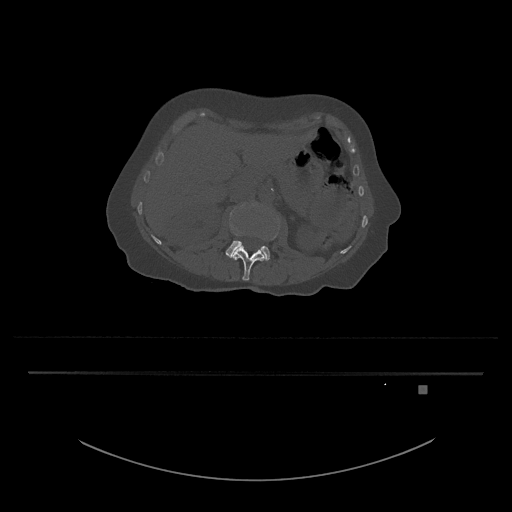
CT including the spine, one axial slice; slice 466 of 797 in the series (ordered by position); 120 kVp; bone window (W 1800 / L 400 HU); 0.5 mm slice thickness; 512 × 512 image matrix, field of view 500 × 500 mm. Female patient, age 57 years. From the clinical record (not read from this slice): primary cancer: cervical.
Structures marked on this image (semi-automatic segmentation, software-assisted and operator-edited):
- L3 vertebra: bounding box (x1, y1, x2, y2) in pixels: (226, 204, 279, 261)